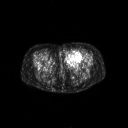
FDG PET of an extremity soft-tissue mass (from a PET/CT study), one axial slice; position 30 of 267 along the scan axis; 3.27 mm slice thickness; 128 × 128 image matrix. Female patient, age 47 years. Case-level facts recorded for this patient, not image findings: histological type: myxofibrosarcoma; grade: intermediate; site of the primary tumour: left thigh.
Outlined on this slice (expert contour drawn on MRI and transferred to this co-registered scan by the dataset authors):
- gross tumour volume including surrounding oedema: bounding box (x1, y1, x2, y2) in pixels: (65, 51, 83, 65)
- gross tumour volume (mass): (66, 51, 82, 63)